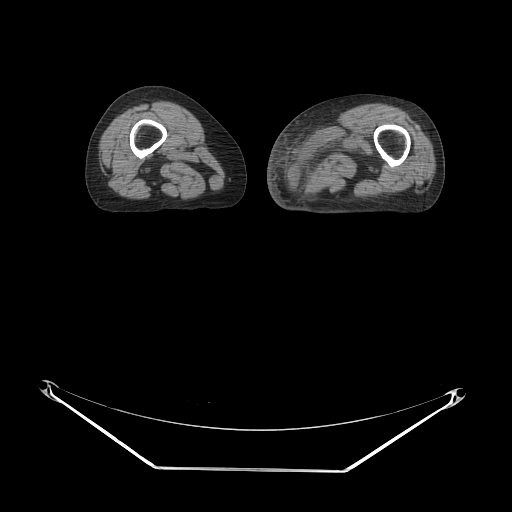
CT of an extremity soft-tissue mass (from a PET/CT study), one axial slice; position 13 of 91 along the scan axis; reconstruction kernel STANDARD; 140 kVp; soft-tissue window (W 400 / L 40 HU); 512 × 512 image matrix, field of view 500 × 500 mm. Female patient. From the clinical record (not read from this slice): histological type: pleomorphic leiomyosarcoma; grade: high; site of the primary tumour: left thigh.
Outlined on this slice (expert contour drawn on MRI and transferred to this co-registered scan by the dataset authors):
- gross tumour volume including surrounding oedema: bounding box <294,123,380,191> (left, top, right, bottom; pixels)
- gross tumour volume (mass): <295,176,316,191>